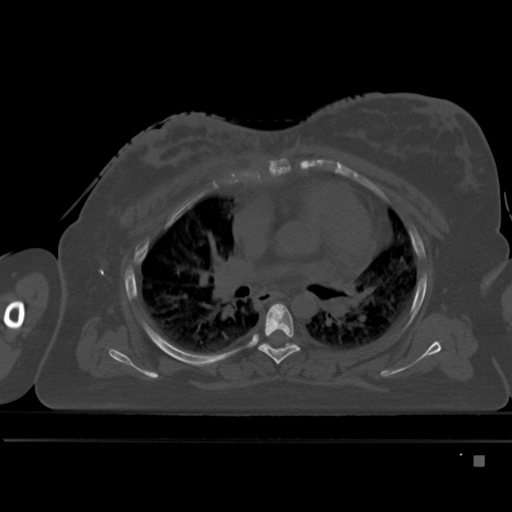
CT including the spine, one axial slice; position 318 of 495 along the scan axis; bone window (W 1800 / L 400 HU); 512 × 512 image matrix, field of view 404 × 404 mm. Female patient, age 33 years. Case-level facts recorded for this patient, not image findings: primary cancer: breast; vertebrae with lytic lesions (as recorded): T1.
Annotated regions visible in this slice (semi-automatic segmentation, software-assisted and operator-edited):
- T5 vertebra: box from (x=258, y=303) to (x=300, y=365) px
- T6 vertebra: (x=261, y=343)–(x=295, y=347)